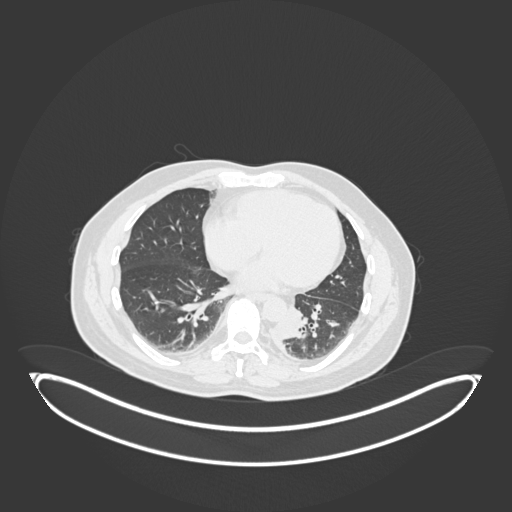
Chest CT, one axial slice; position 65 of 258 along the scan axis; 120 kVp; lung window (W 1500 / L -600 HU); 1 mm slice thickness; 512 × 512 image matrix, field of view 500 × 500 mm. Male patient, age 54 years. Case-level facts recorded for this patient, not image findings: clinical TNM (as recorded): T3 N0 M0.
Annotated regions visible in this slice (rectangle marked by the reading radiologist):
- lung tumour (recorded histology: squamous cell carcinoma): bounding box (x1, y1, x2, y2) in pixels: (270, 308, 308, 345)